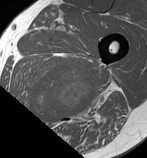
MRI of an extremity soft-tissue mass, one axial slice; position 77 of 86 along the scan axis; MR volume resampled by the dataset authors to the PET/CT grid (not the native acquisition matrix); 3.27 mm slice thickness; 147 × 158 image matrix. Male patient. Case-level facts recorded for this patient, not image findings: histological type: undifferentiated pleomorphic liposarcoma; grade: high; site of the primary tumour: left thigh.
Annotated regions visible in this slice (expert contour drawn on MRI and transferred to this co-registered scan by the dataset authors):
- gross tumour volume including surrounding oedema: bounding box [x1, y1, x2, y2] px = [25, 65, 104, 123]
- gross tumour volume (mass): [30, 67, 95, 121]